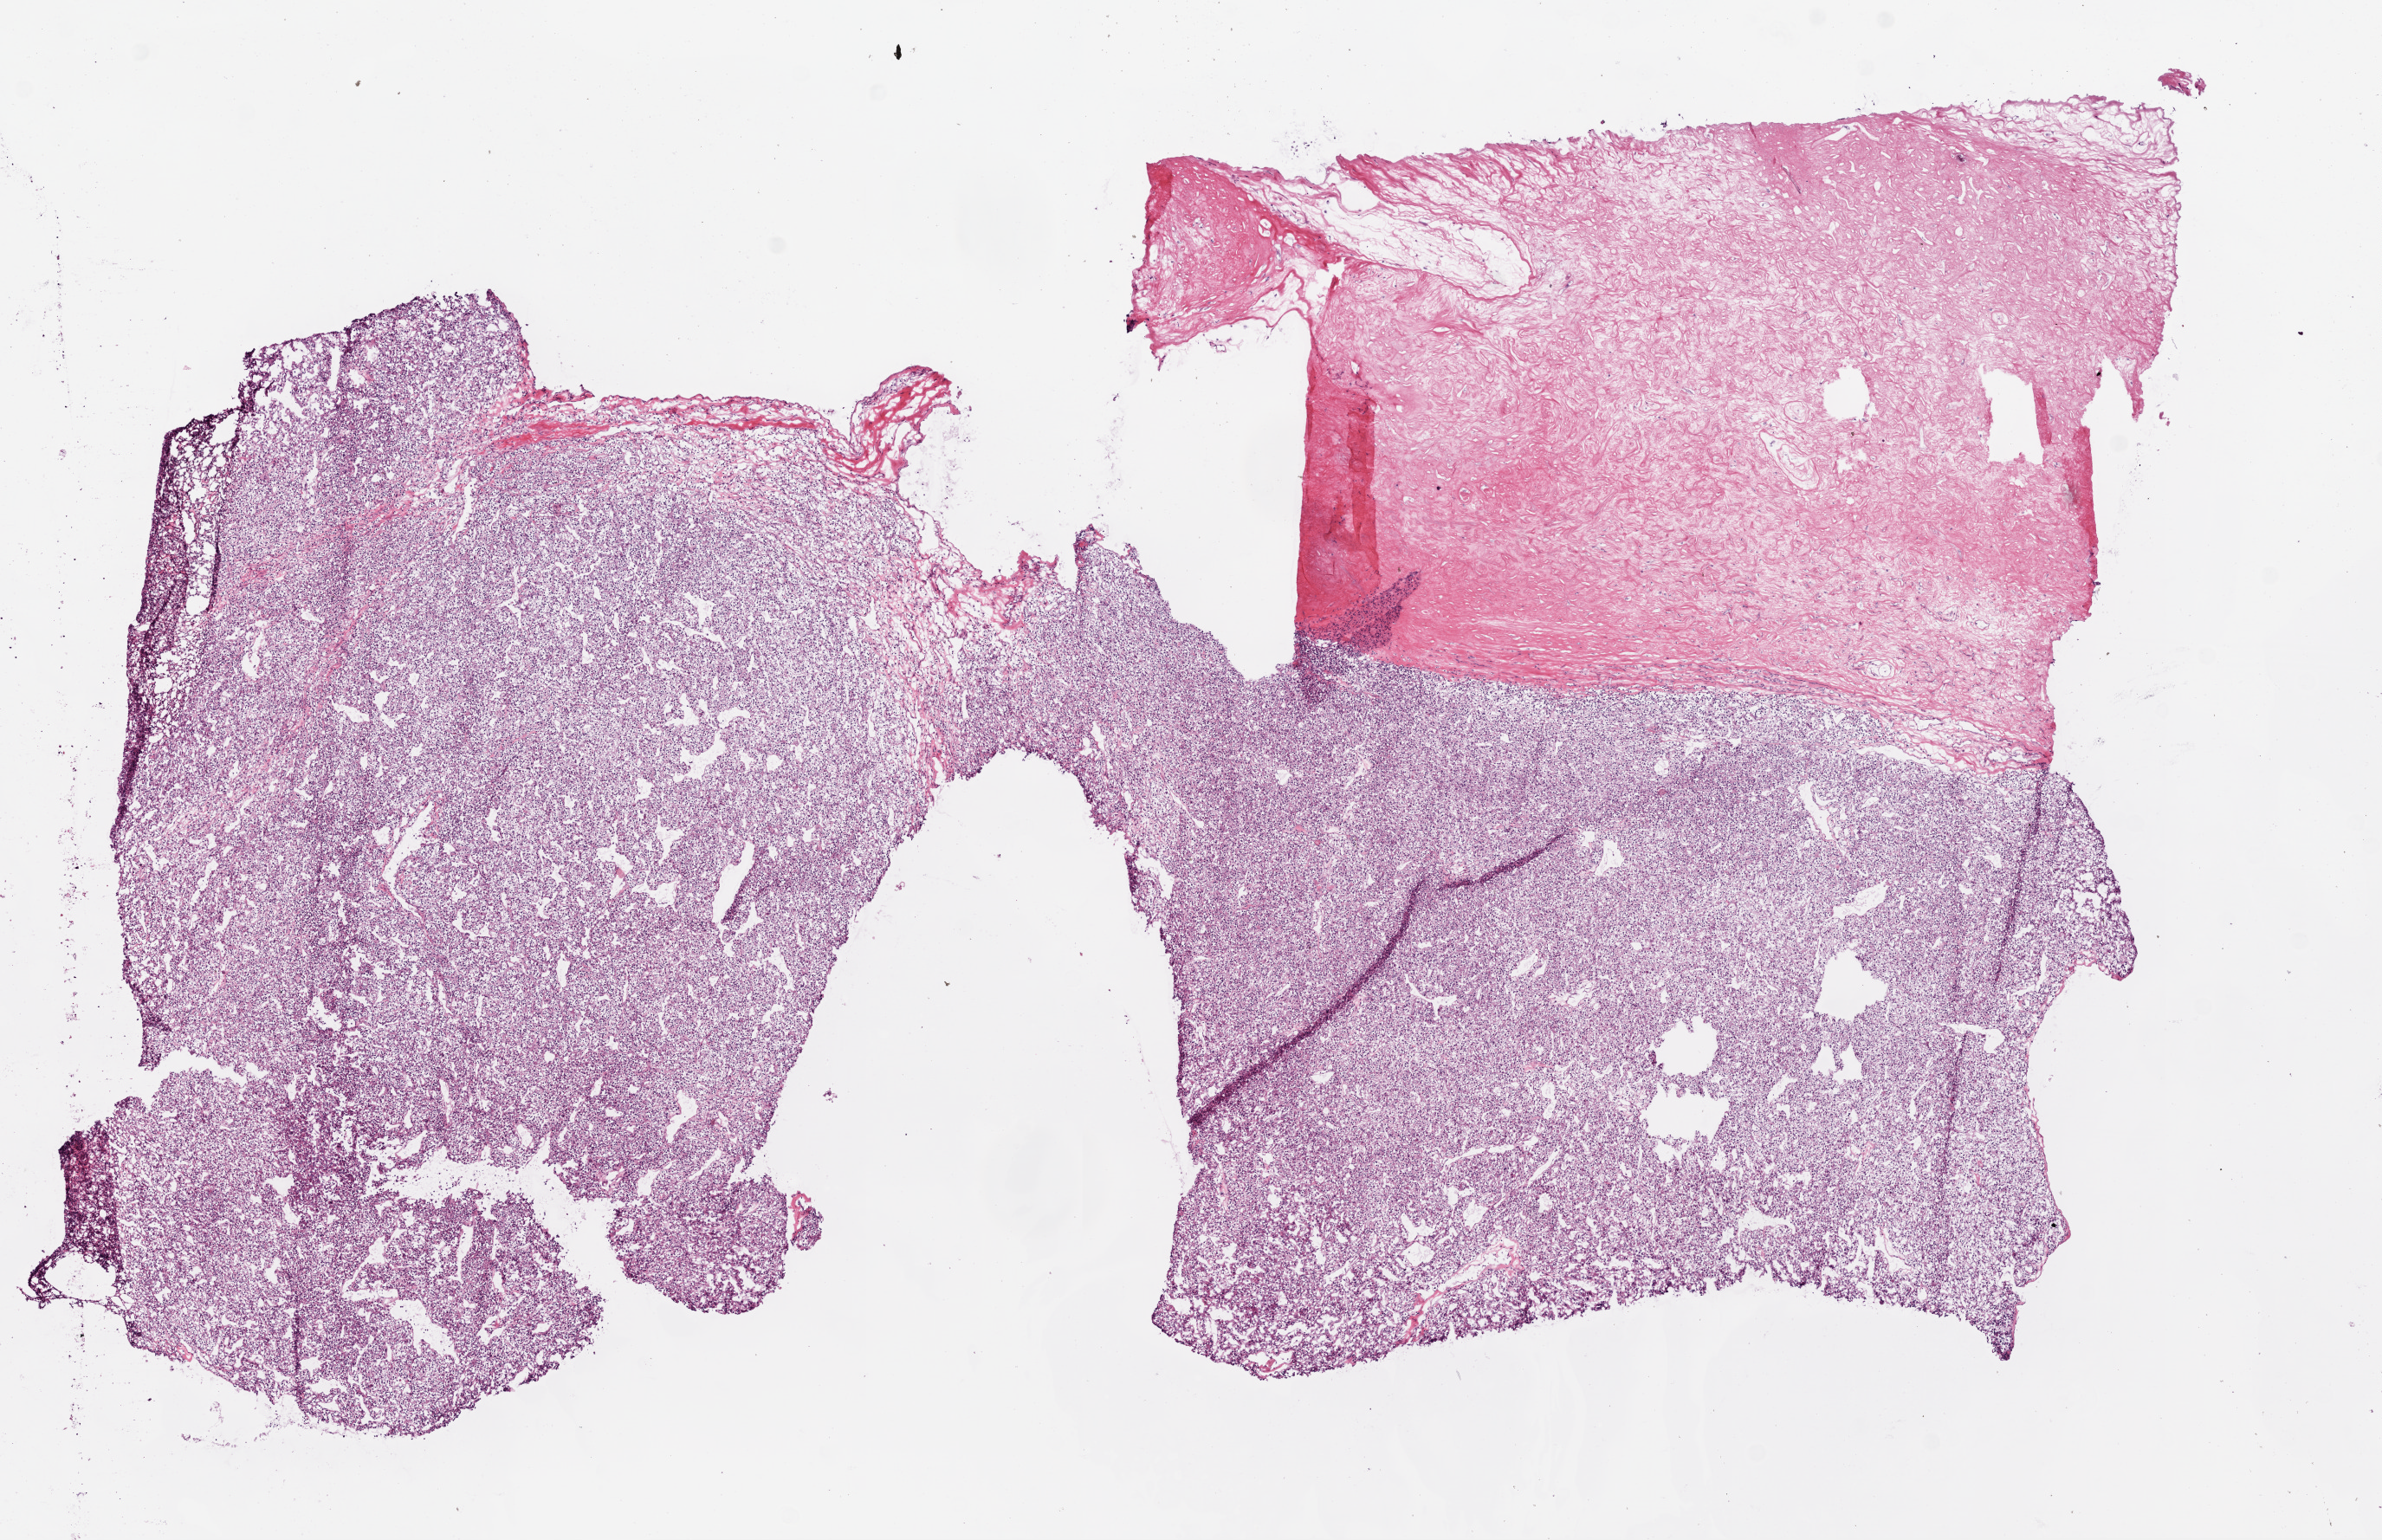
Whole-slide histology image, H&E-stained — shown as a low-resolution overview of the whole scanned area (about 11.0 x 7.1 mm, acquisition: 20x scan), frozen section, sample: primary tumour, kidney. Patient: female, age at initial diagnosis 51 years. Histologic grade: G2 (moderately differentiated). Slide review estimates, as recorded: tumour cells 60%, tumour nuclei 90%, normal cells 0%, stromal cells 10%, necrosis 30%.
- AJCC pathologic stage: III (6th edition)
- histologic diagnosis: Clear cell adenocarcinoma, NOS